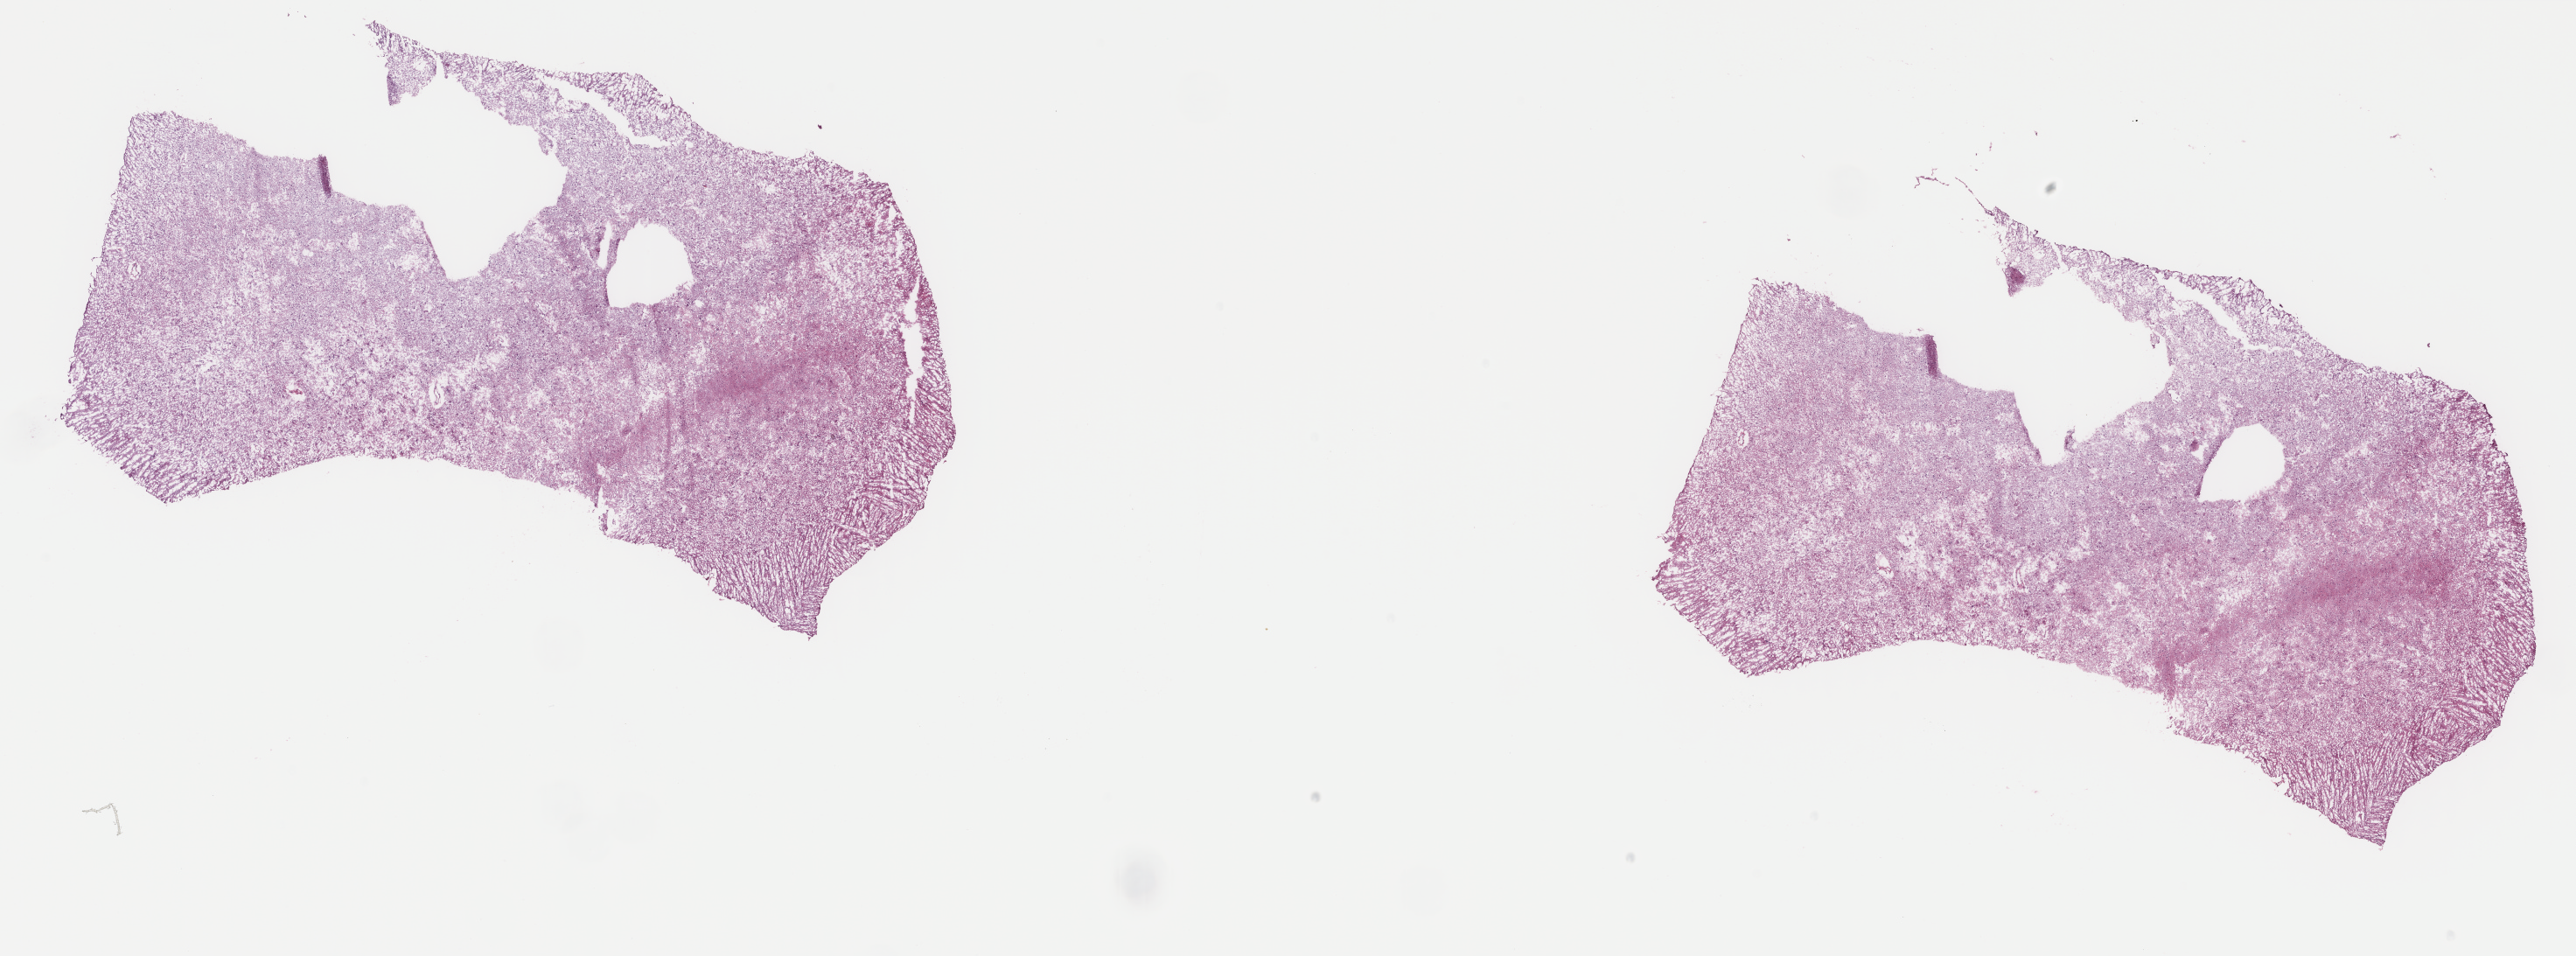
Hematoxylin and eosin (H&E) stained whole-slide image, shown as a low-resolution overview of the whole scanned area (about 23.4 x 8.7 mm, acquisition: 40x scan); frozen section from the top of the tissue portion; primary tumour sample from the brain. Male patient; age at initial diagnosis 66 years. Slide review estimates, as recorded: tumour cells 30%, tumour nuclei 80%.
Pathologic diagnosis: Mixed glioma (cerebrum).